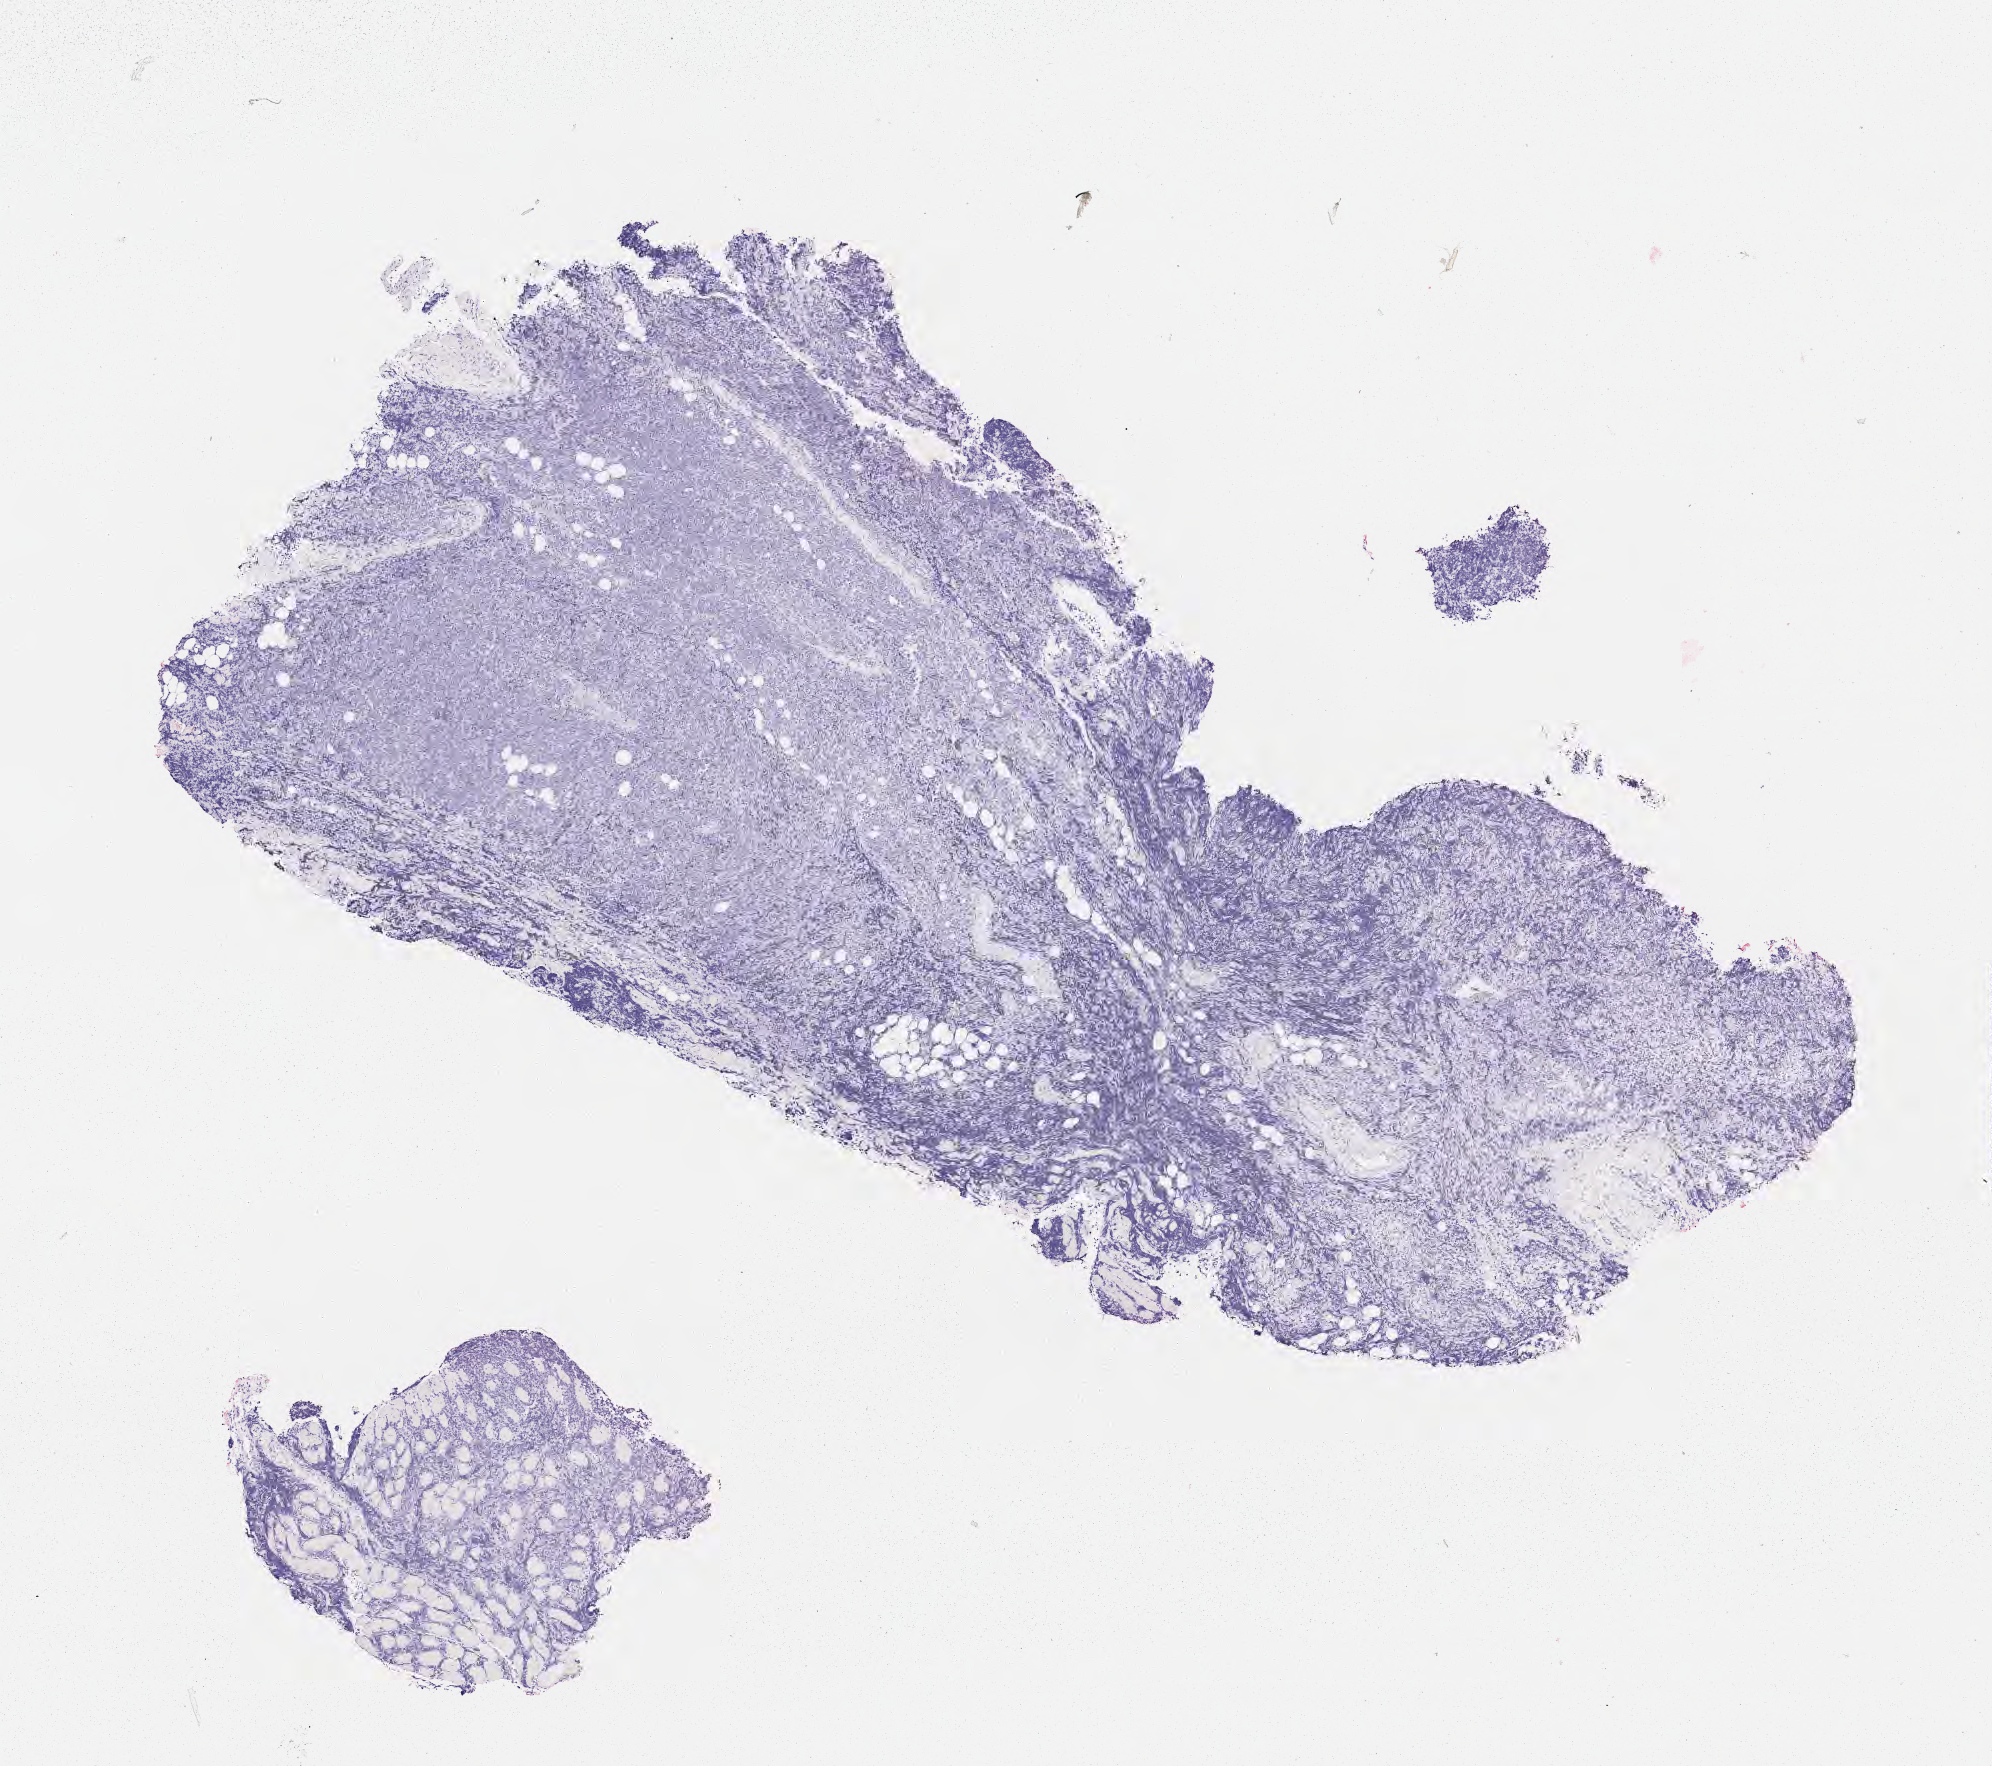
In-situ hybridisation whole-slide image, Epstein–Barr virus-encoded RNA (EBER) probe — low-resolution overview of the scanned area, about 8.0 x 7.1 mm; tumor tissue. Male patient, 67 years old.
• histologic diagnosis: Diffuse large B-cell lymphoma, NOS